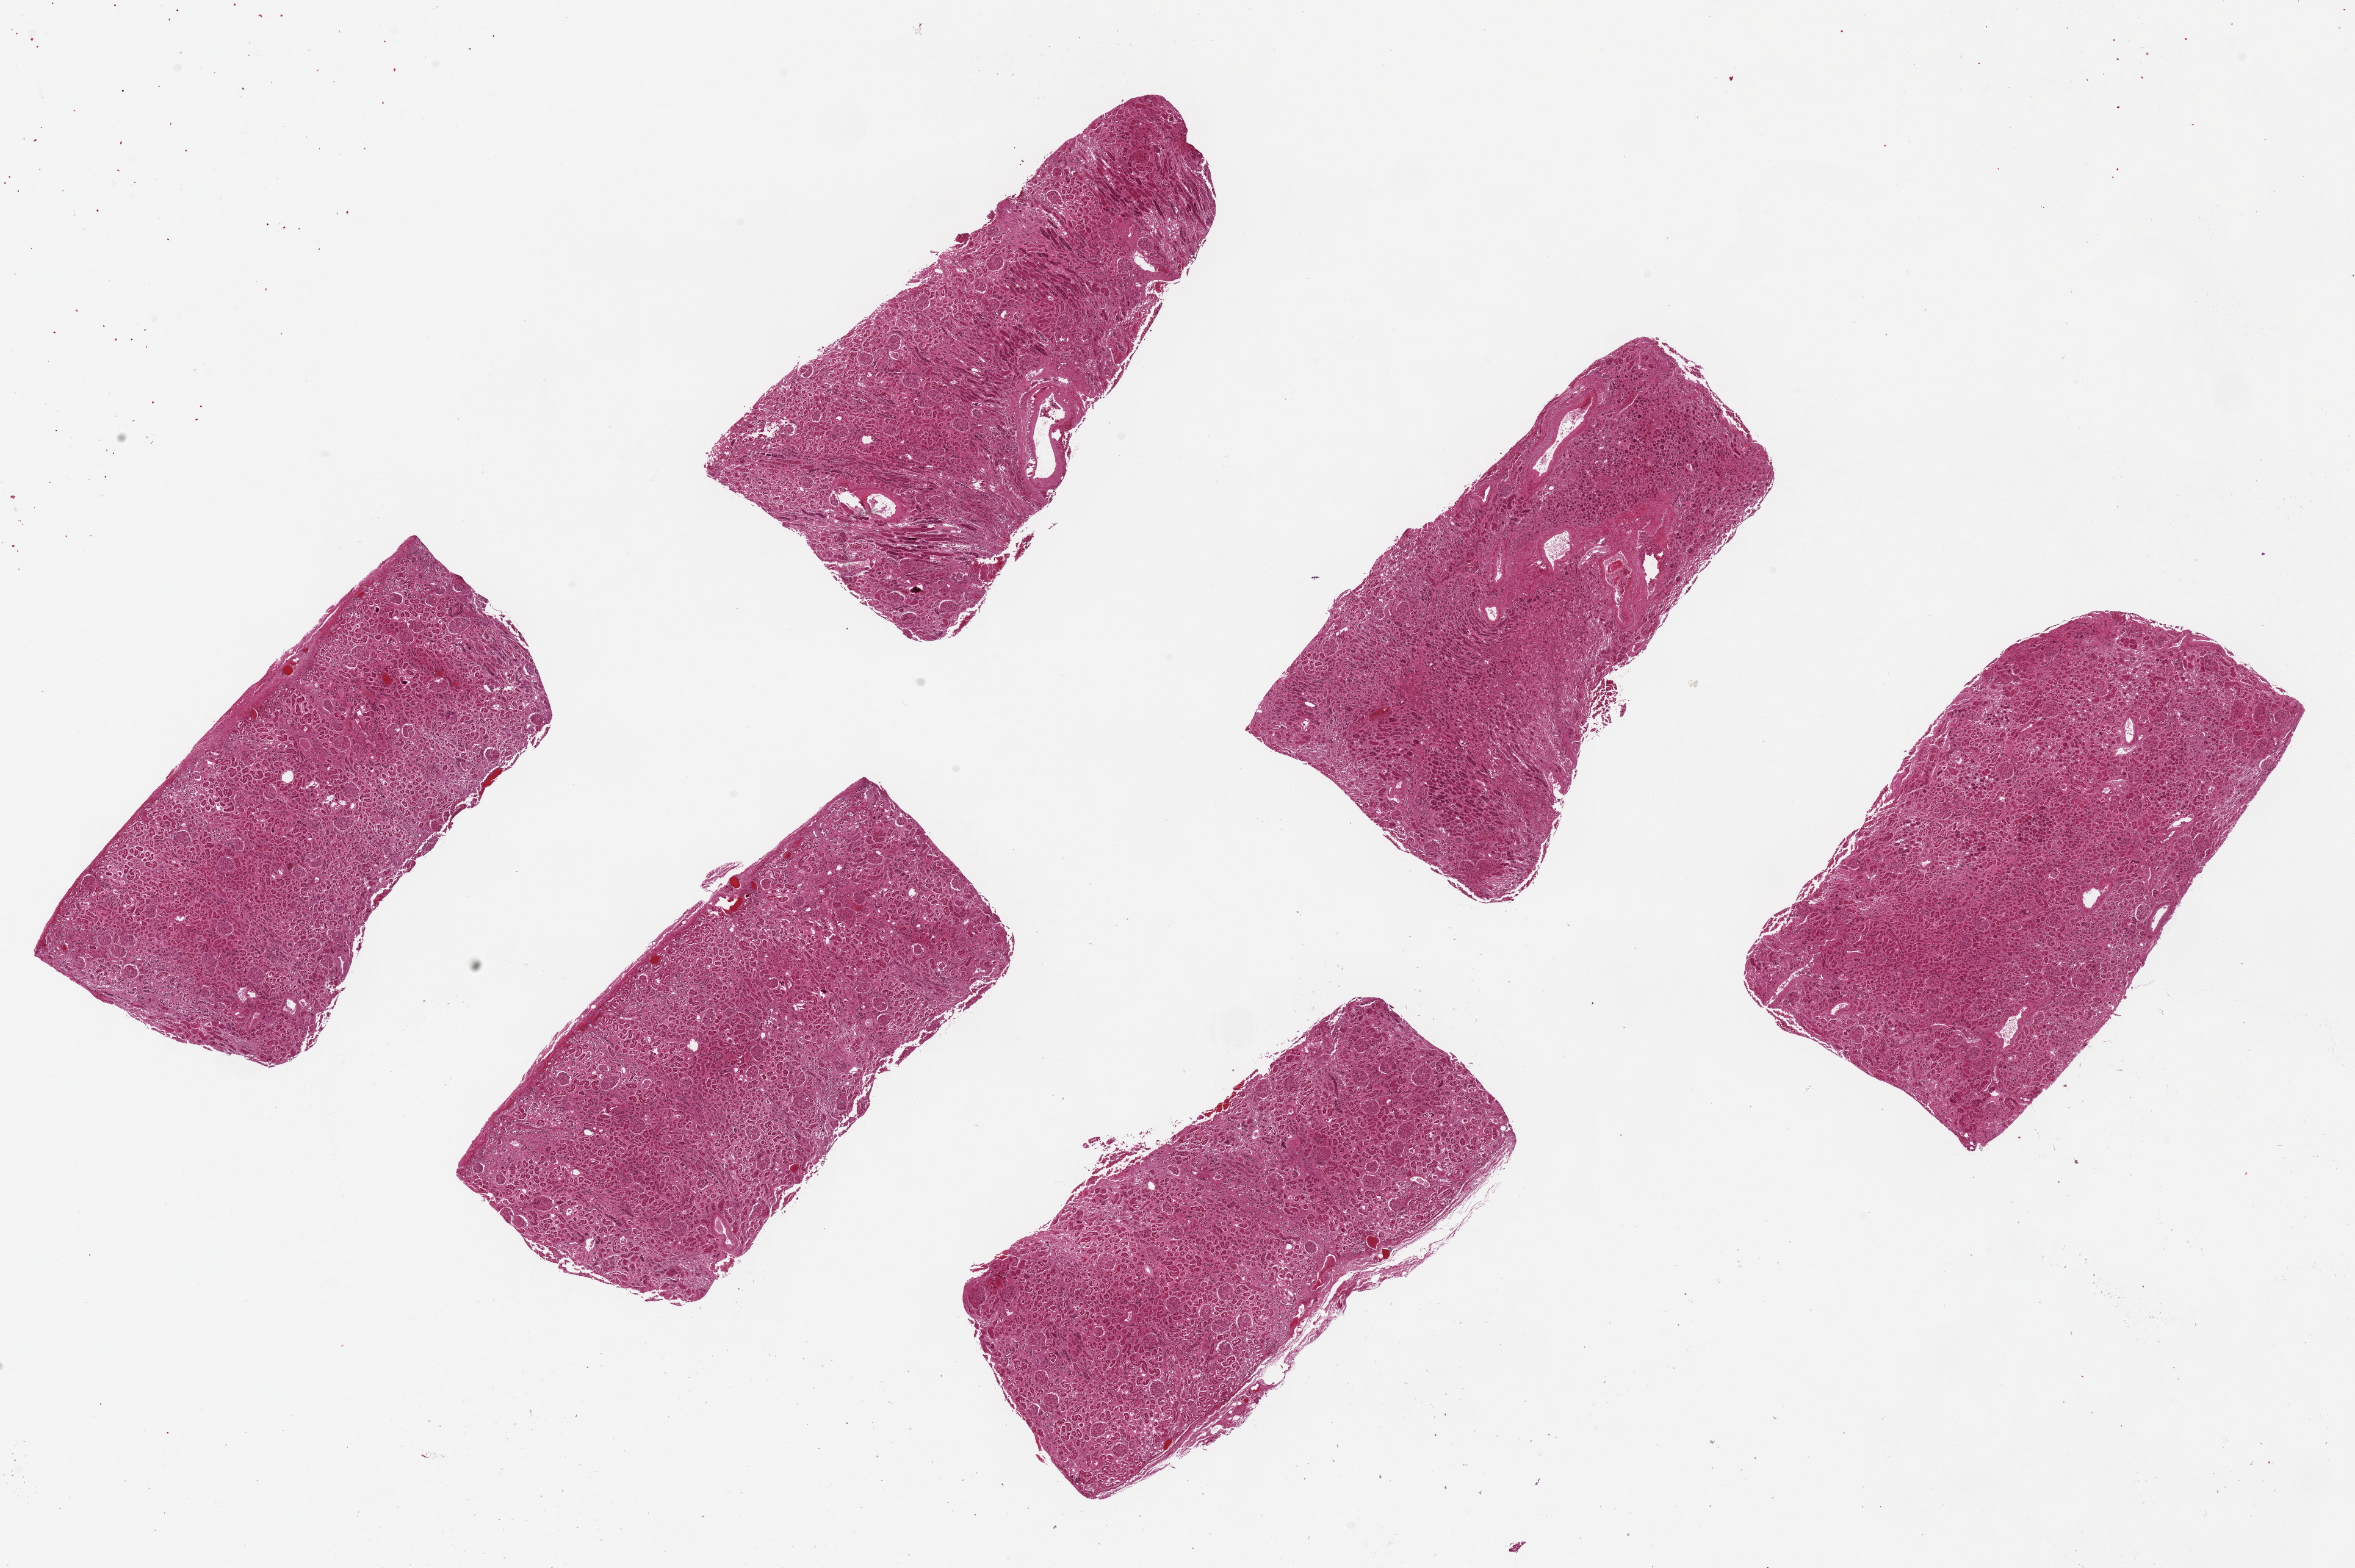
H&E whole-slide image — shown as a low-resolution overview of the whole scanned area (about 30.5 x 20.3 mm), PAXgene-fixed, paraffin-embedded tissue, section of renal cortex (target tissue), tissue donor sample. Female donor.
Review note (as recorded): 6 pieces ~7x3mm, badly autolyzed.